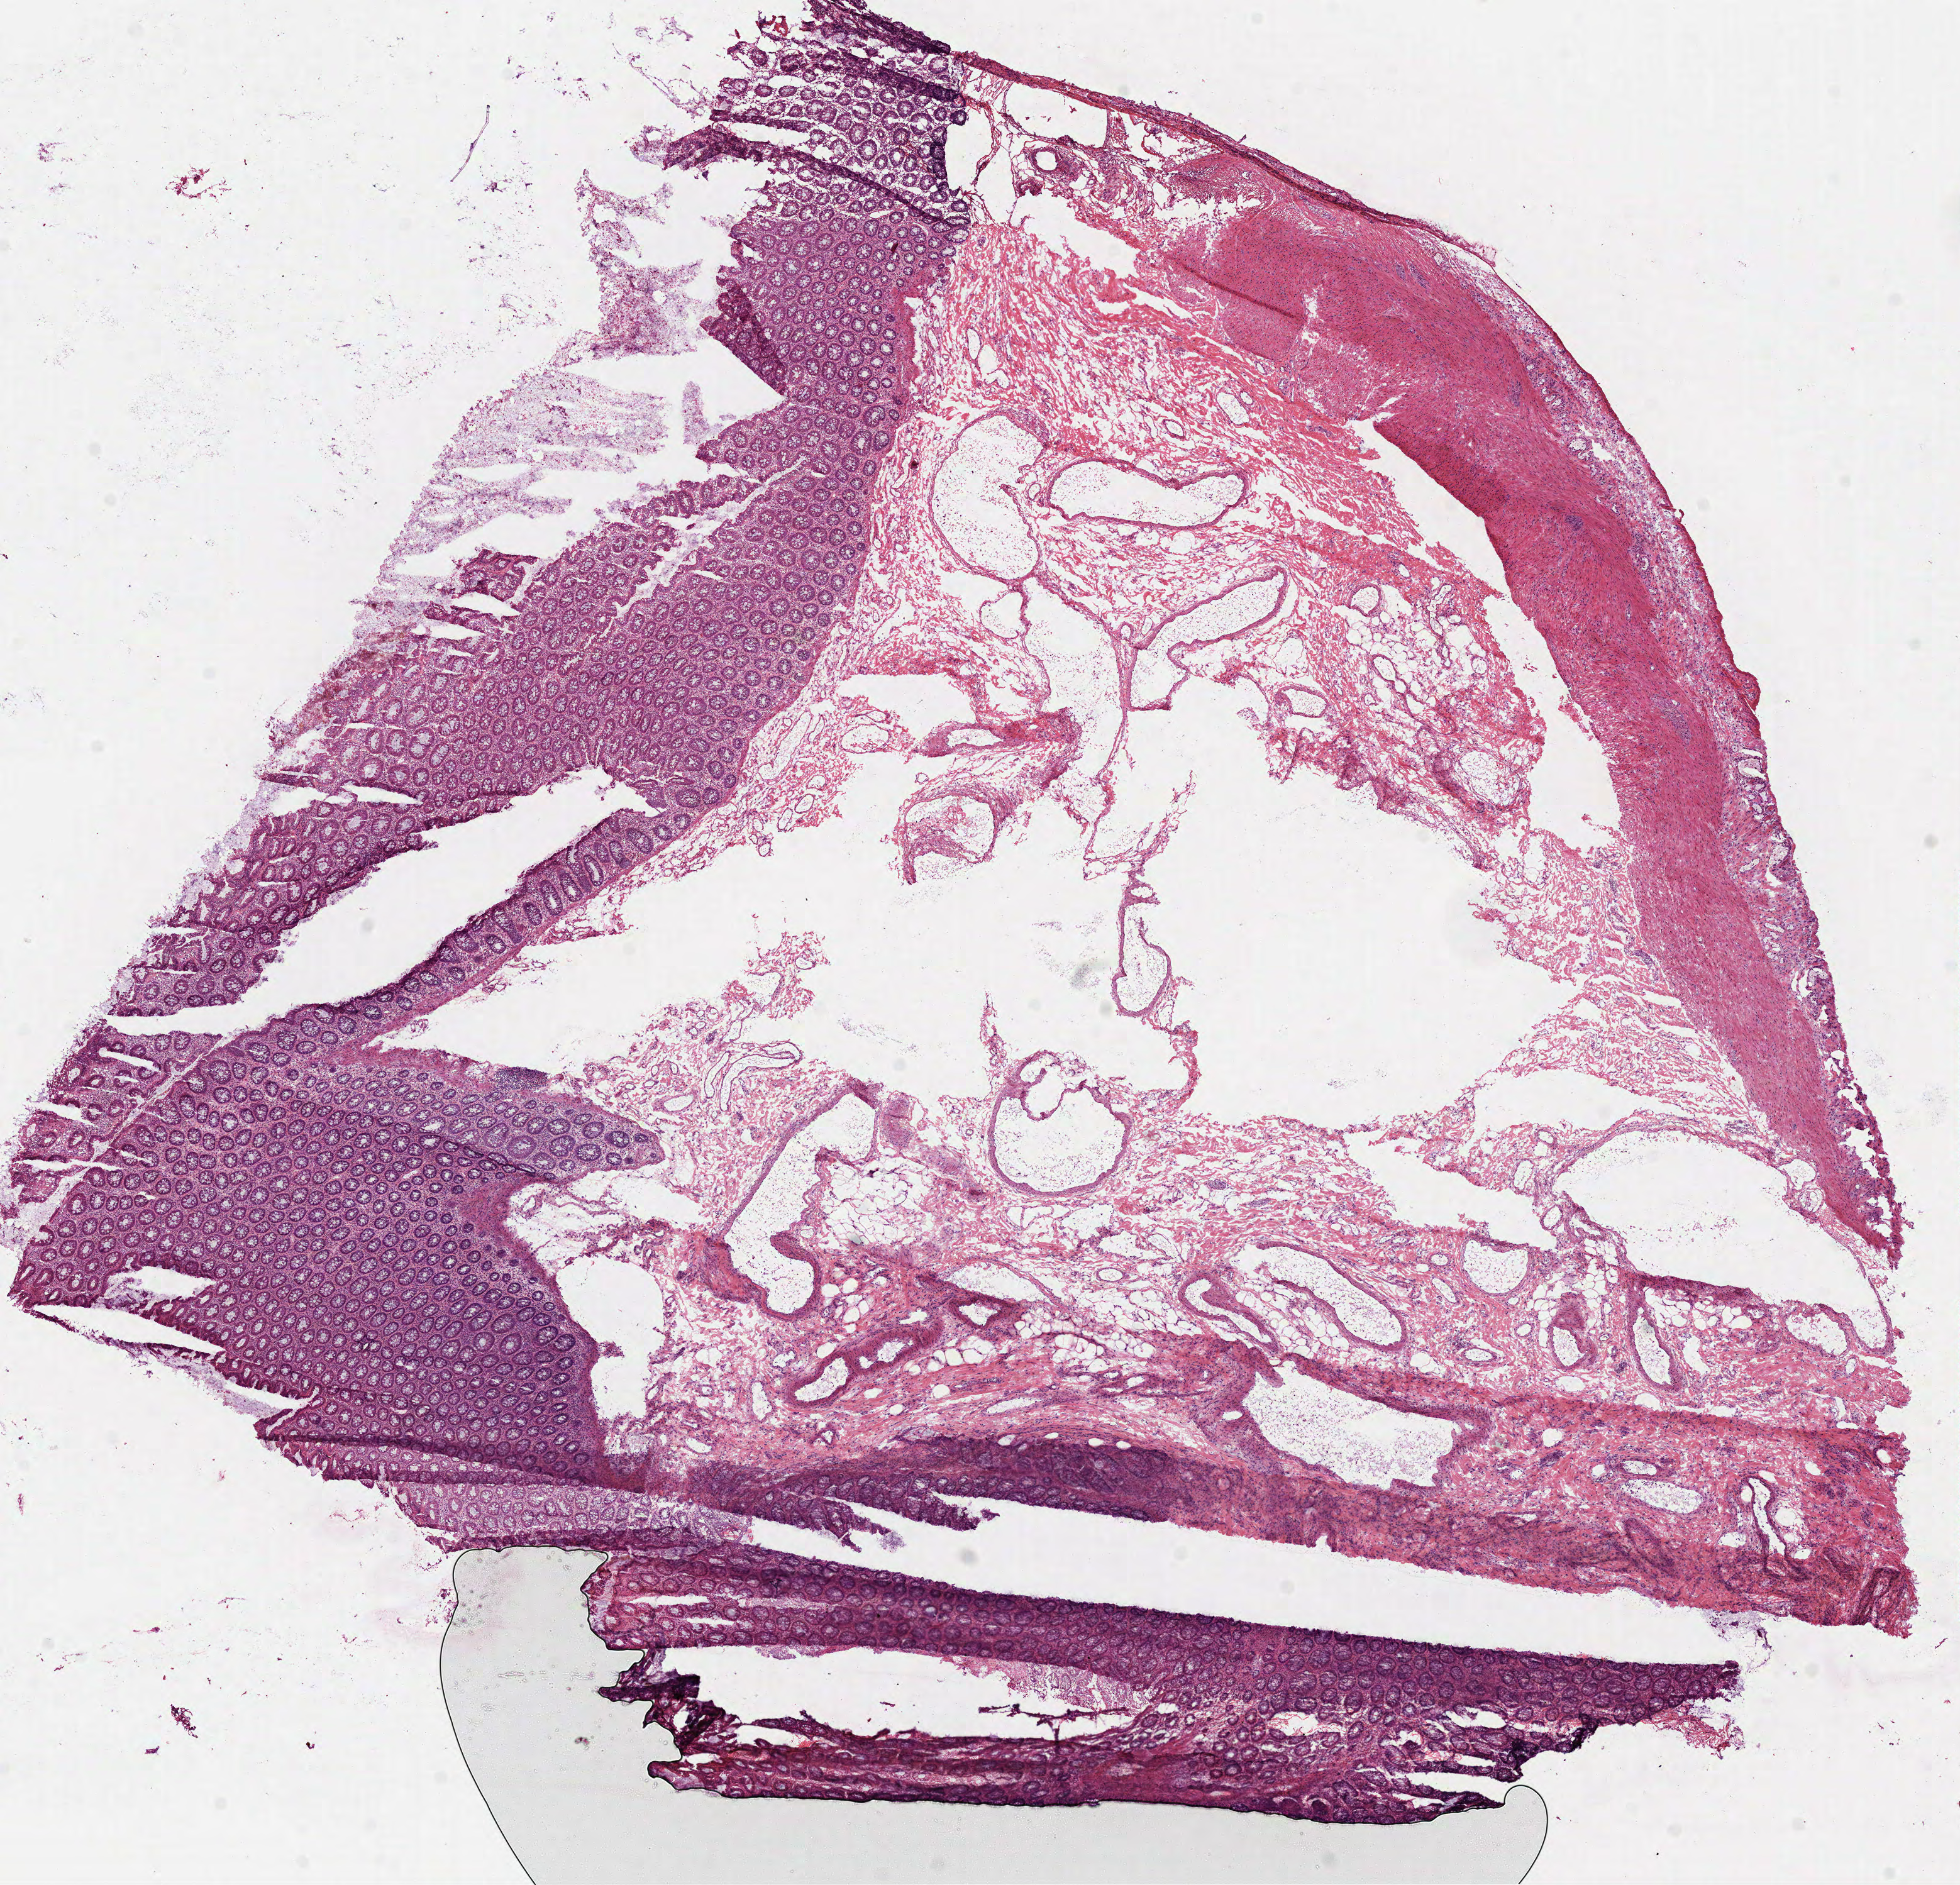
H&E-stained whole-slide image, whole scanned area (about 12.6 x 12.1 mm) shown as a low-resolution overview, frozen section from the top of the tissue portion, sample: solid tissue normal (non-tumour tissue), colon. Patient: male, age at initial diagnosis 72 years.
- this section: solid tissue normal sample (biorepository sample class)
- patient diagnosis: Adenocarcinoma, NOS (cecum)